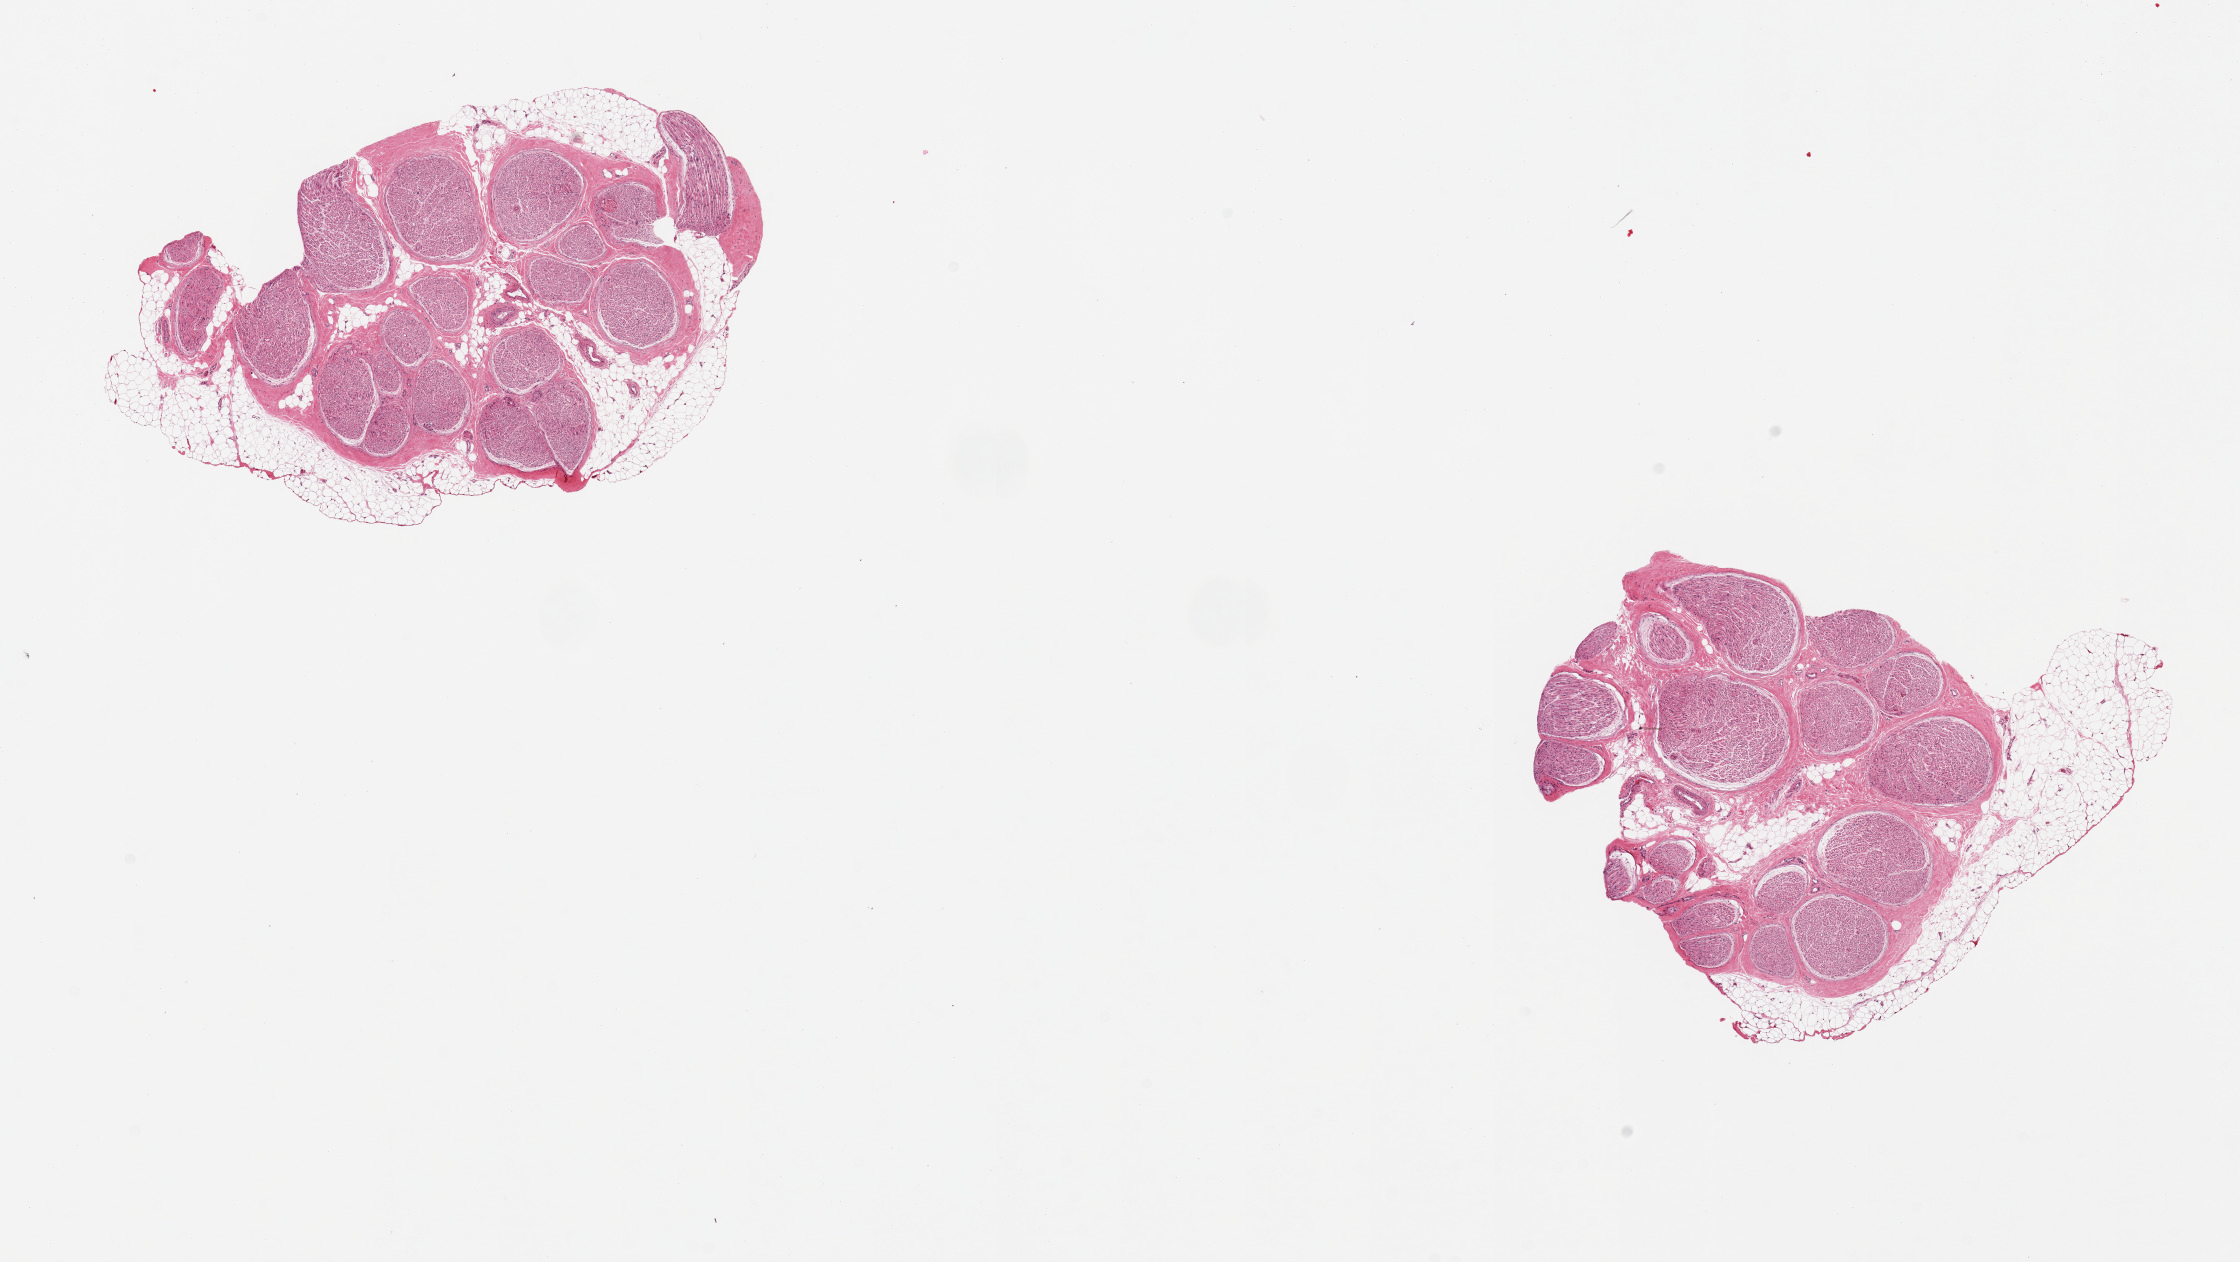
Digitized haematoxylin and eosin-stained section, brightfield — shown as a low-resolution overview of the whole scanned area (about 17.7 x 10.0 mm). PAXgene-fixed, paraffin-embedded tissue. Section of tibial nerve (target tissue). Tissue donor sample. Female donor.
Review note (as recorded): 2 pieces; includes partial rim of external fat (~20%).